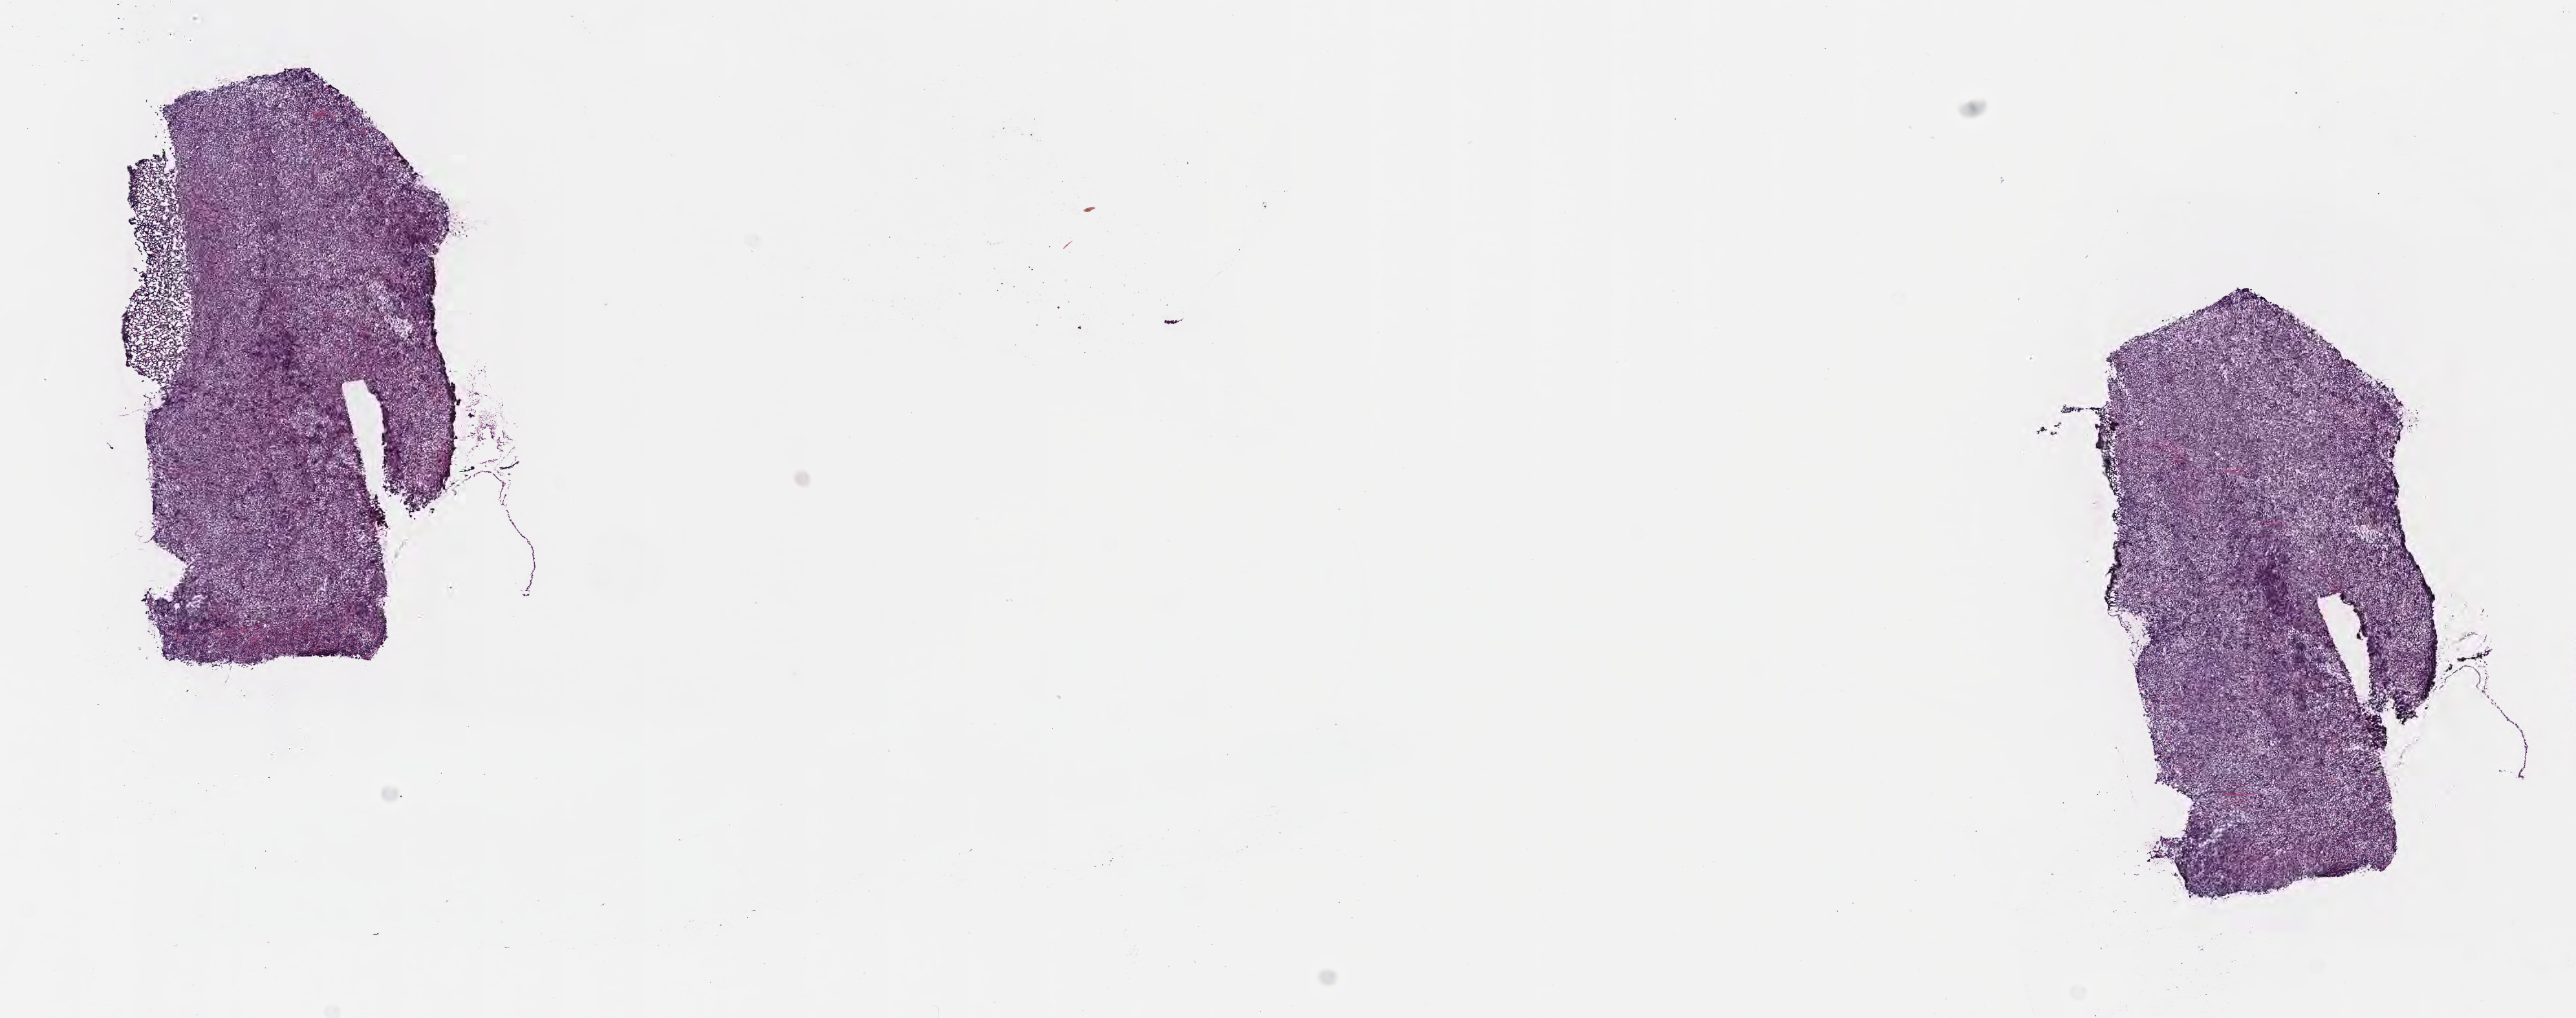
Digitized H&E-stained section — a low-resolution overview of the entire scanned area, about 16.1 x 6.4 mm; cryosection; specimen: primary tumor; anatomic site: cranium. Male, age 5 years at initial diagnosis. Pathologist review of this section (percent, as recorded): tumor cells 90%, tumor nuclei 90%, stromal cells 5%, necrosis 5%, normal cells 0%. Inflammatory infiltration, as recorded: lymphocyte infiltration 60%, monocyte infiltration 15%, neutrophil infiltration 5%.
- histologic diagnosis: Burkitt lymphoma, NOS
- Ann Arbor stage (patient): Stage IV
- section: bottom of the tissue portion